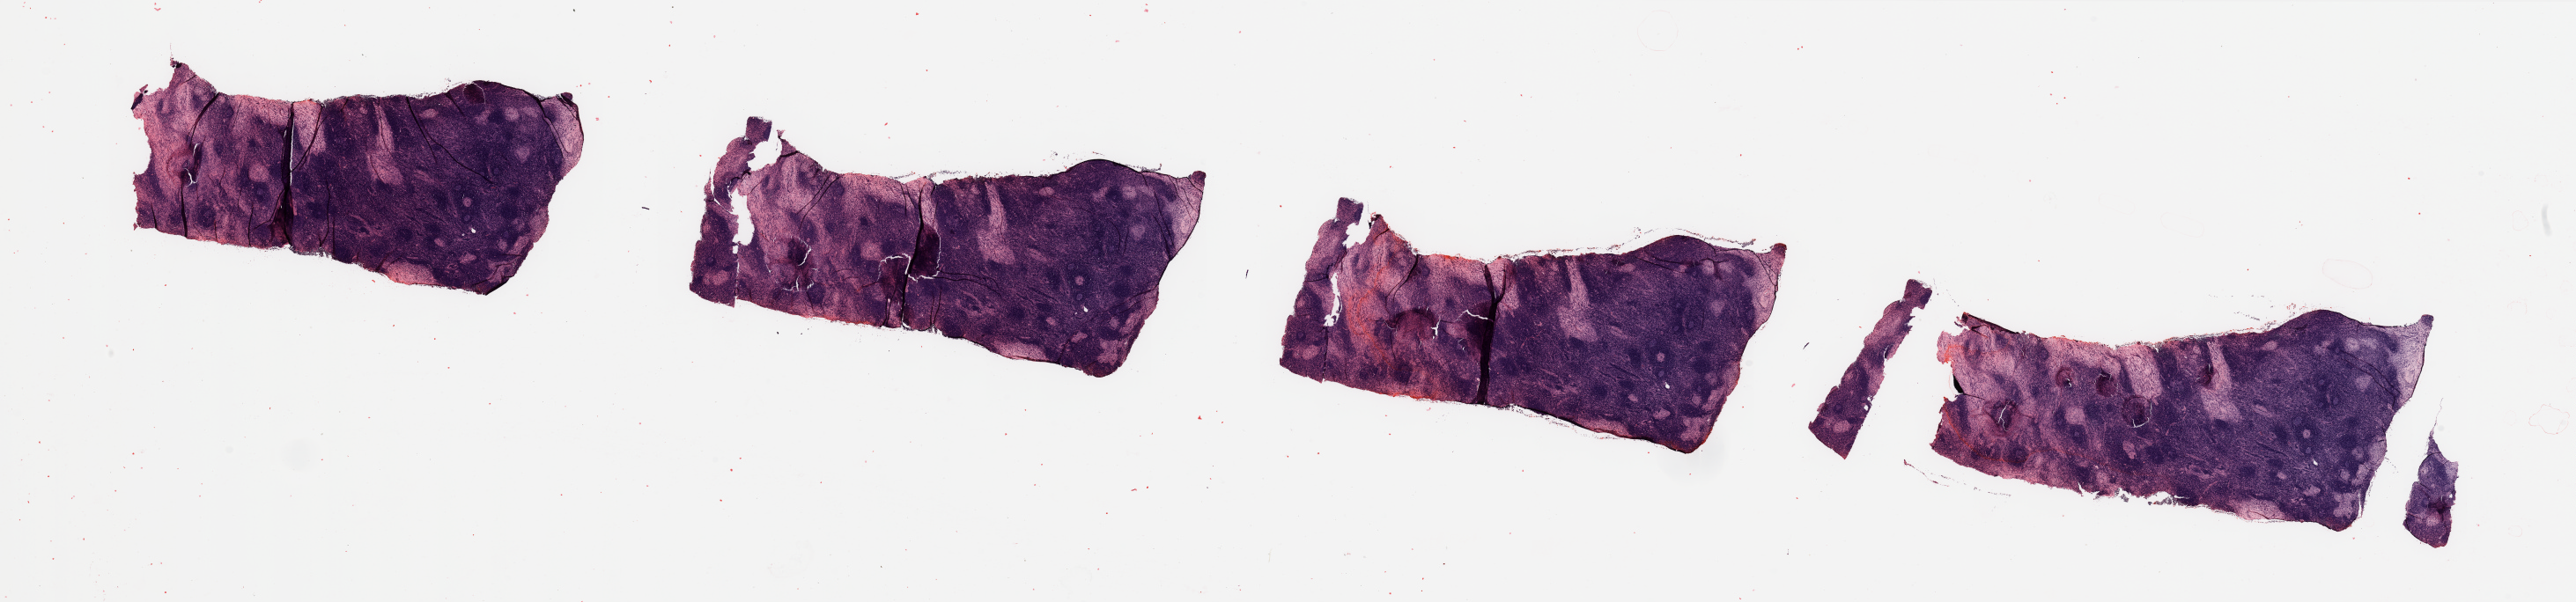
Whole-slide histology image, H&E-stained — whole scanned area (about 46.3 x 10.8 mm) shown as a low-resolution overview. Tumour tissue sample, sampled site: lymph node. Female, 58 y/o.
Patient diagnosis: Malignant melanoma, NOS.